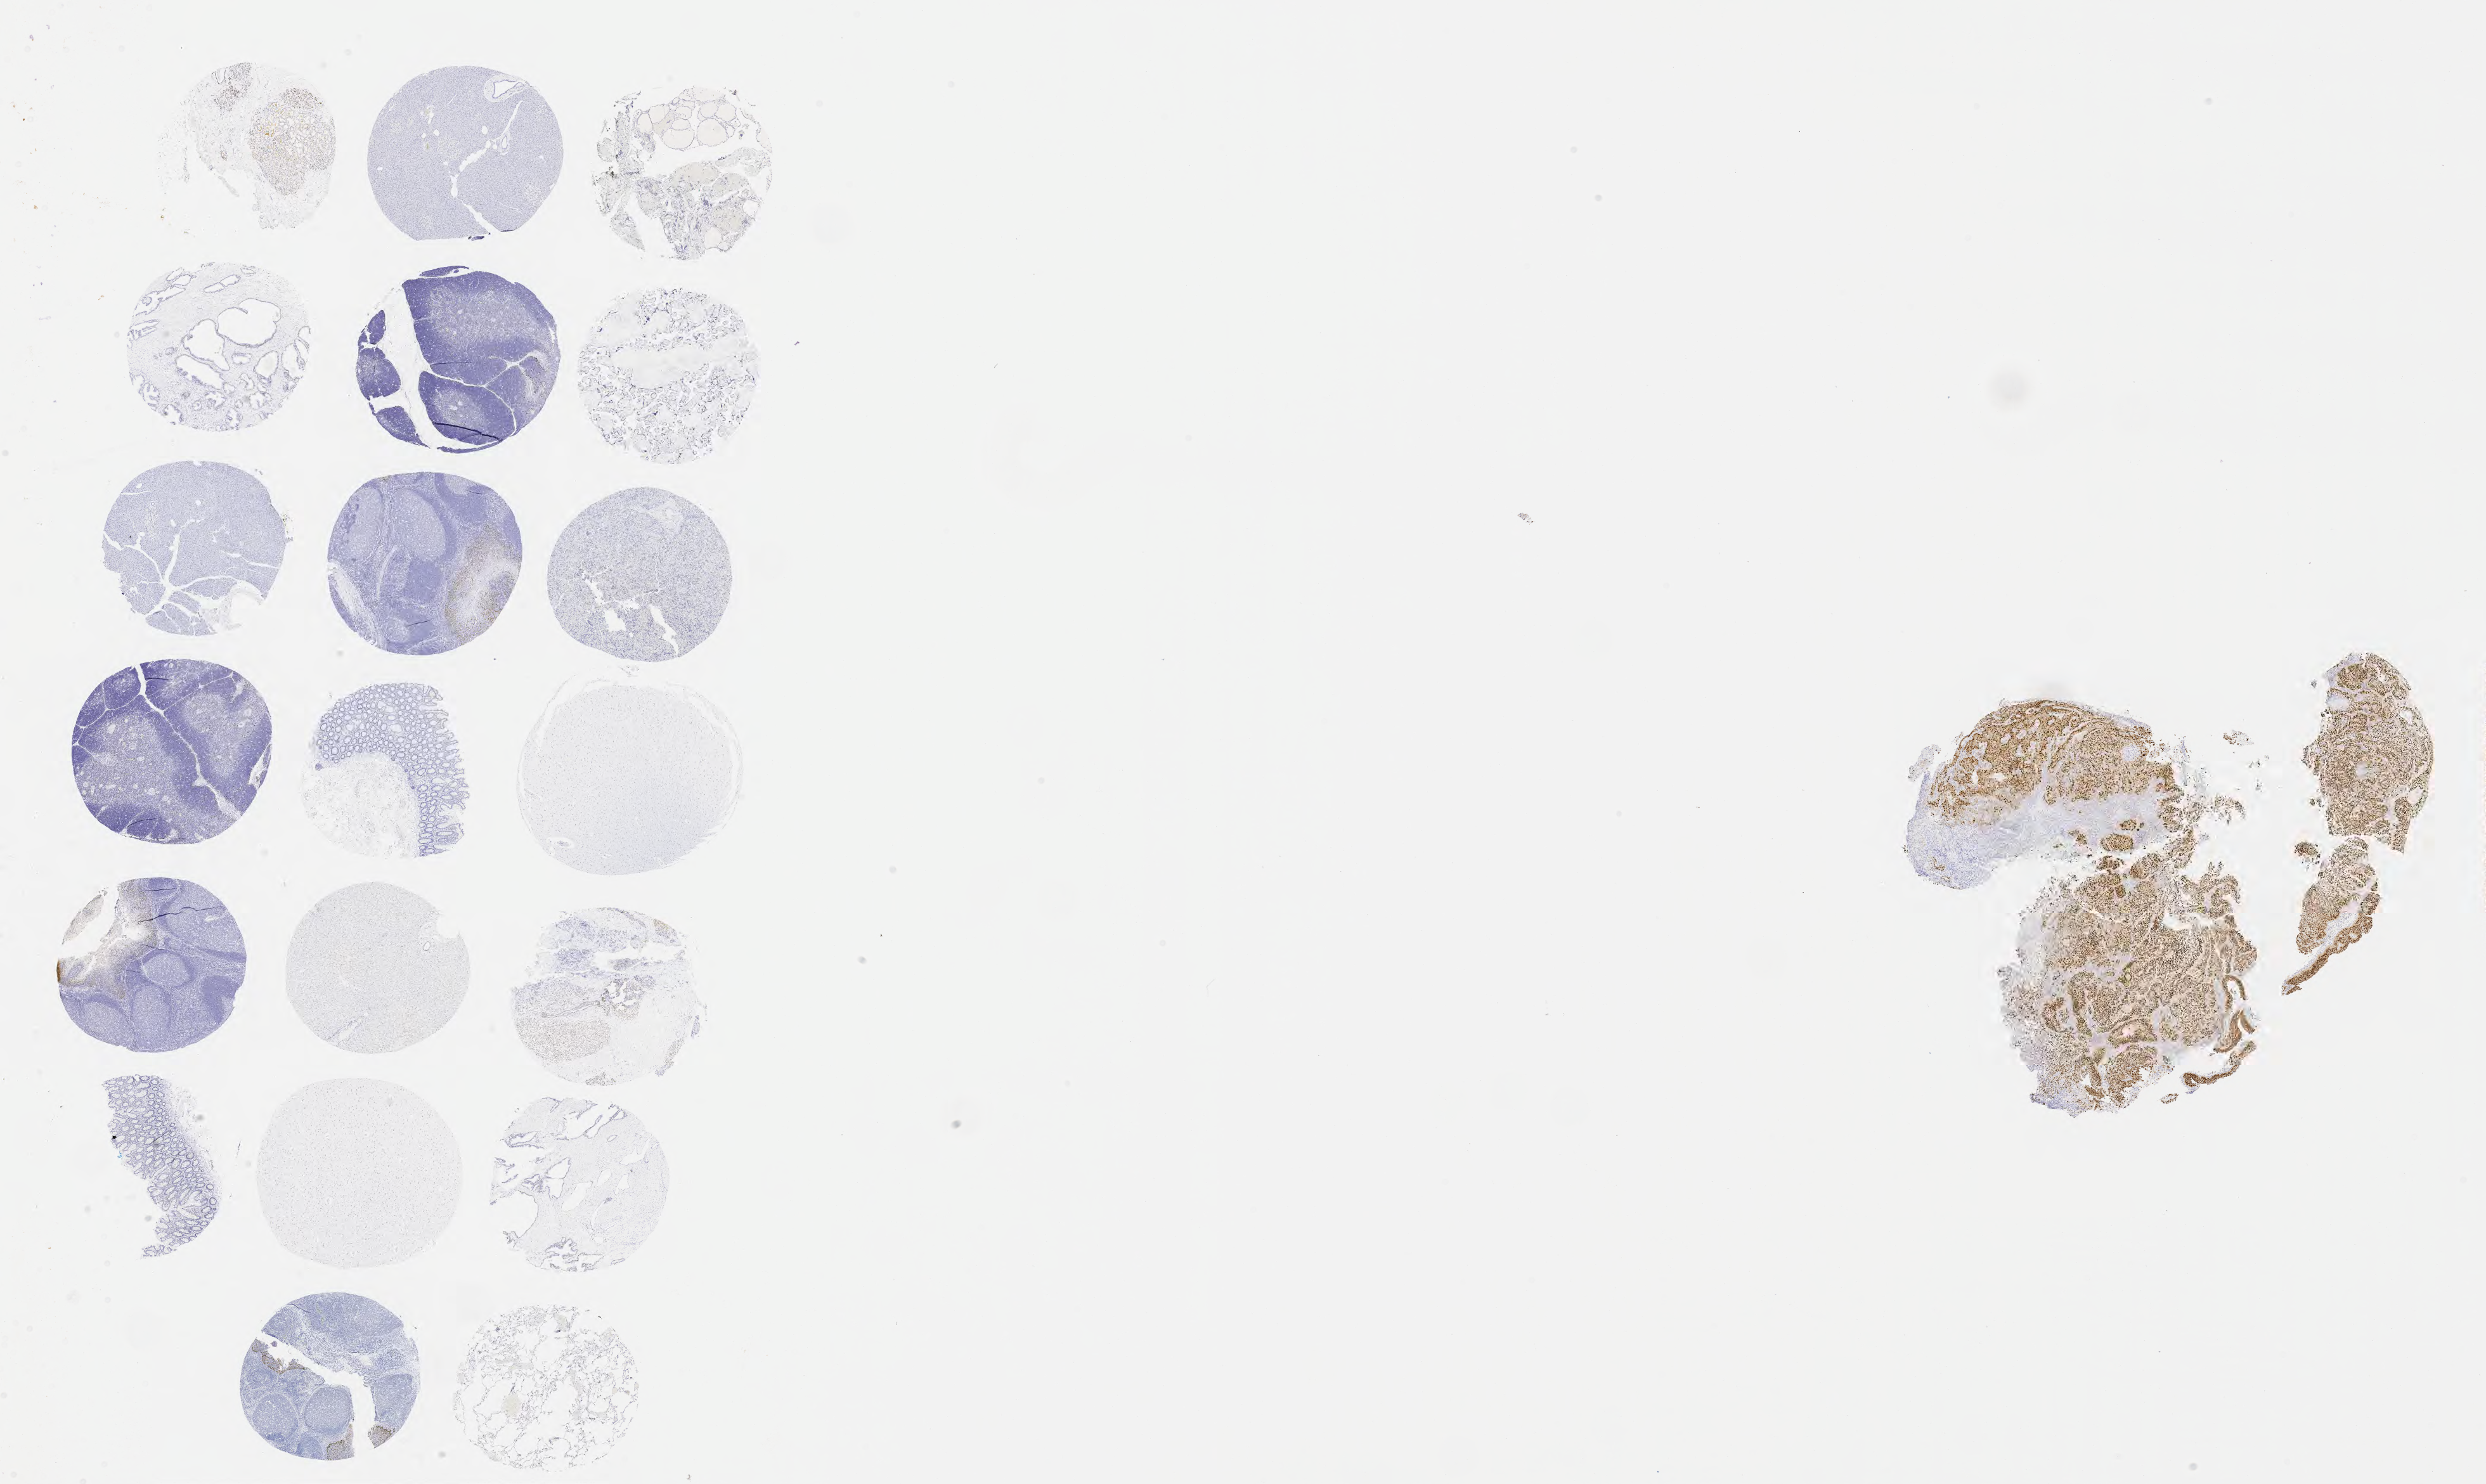
IHC for p63, whole-slide image, shown as a low-resolution overview of the whole scanned area (about 31.7 x 18.9 mm), tumor tissue, site: cervix. Female patient, aged 56.
Histologic diagnosis: Adenocarcinoma, NOS.